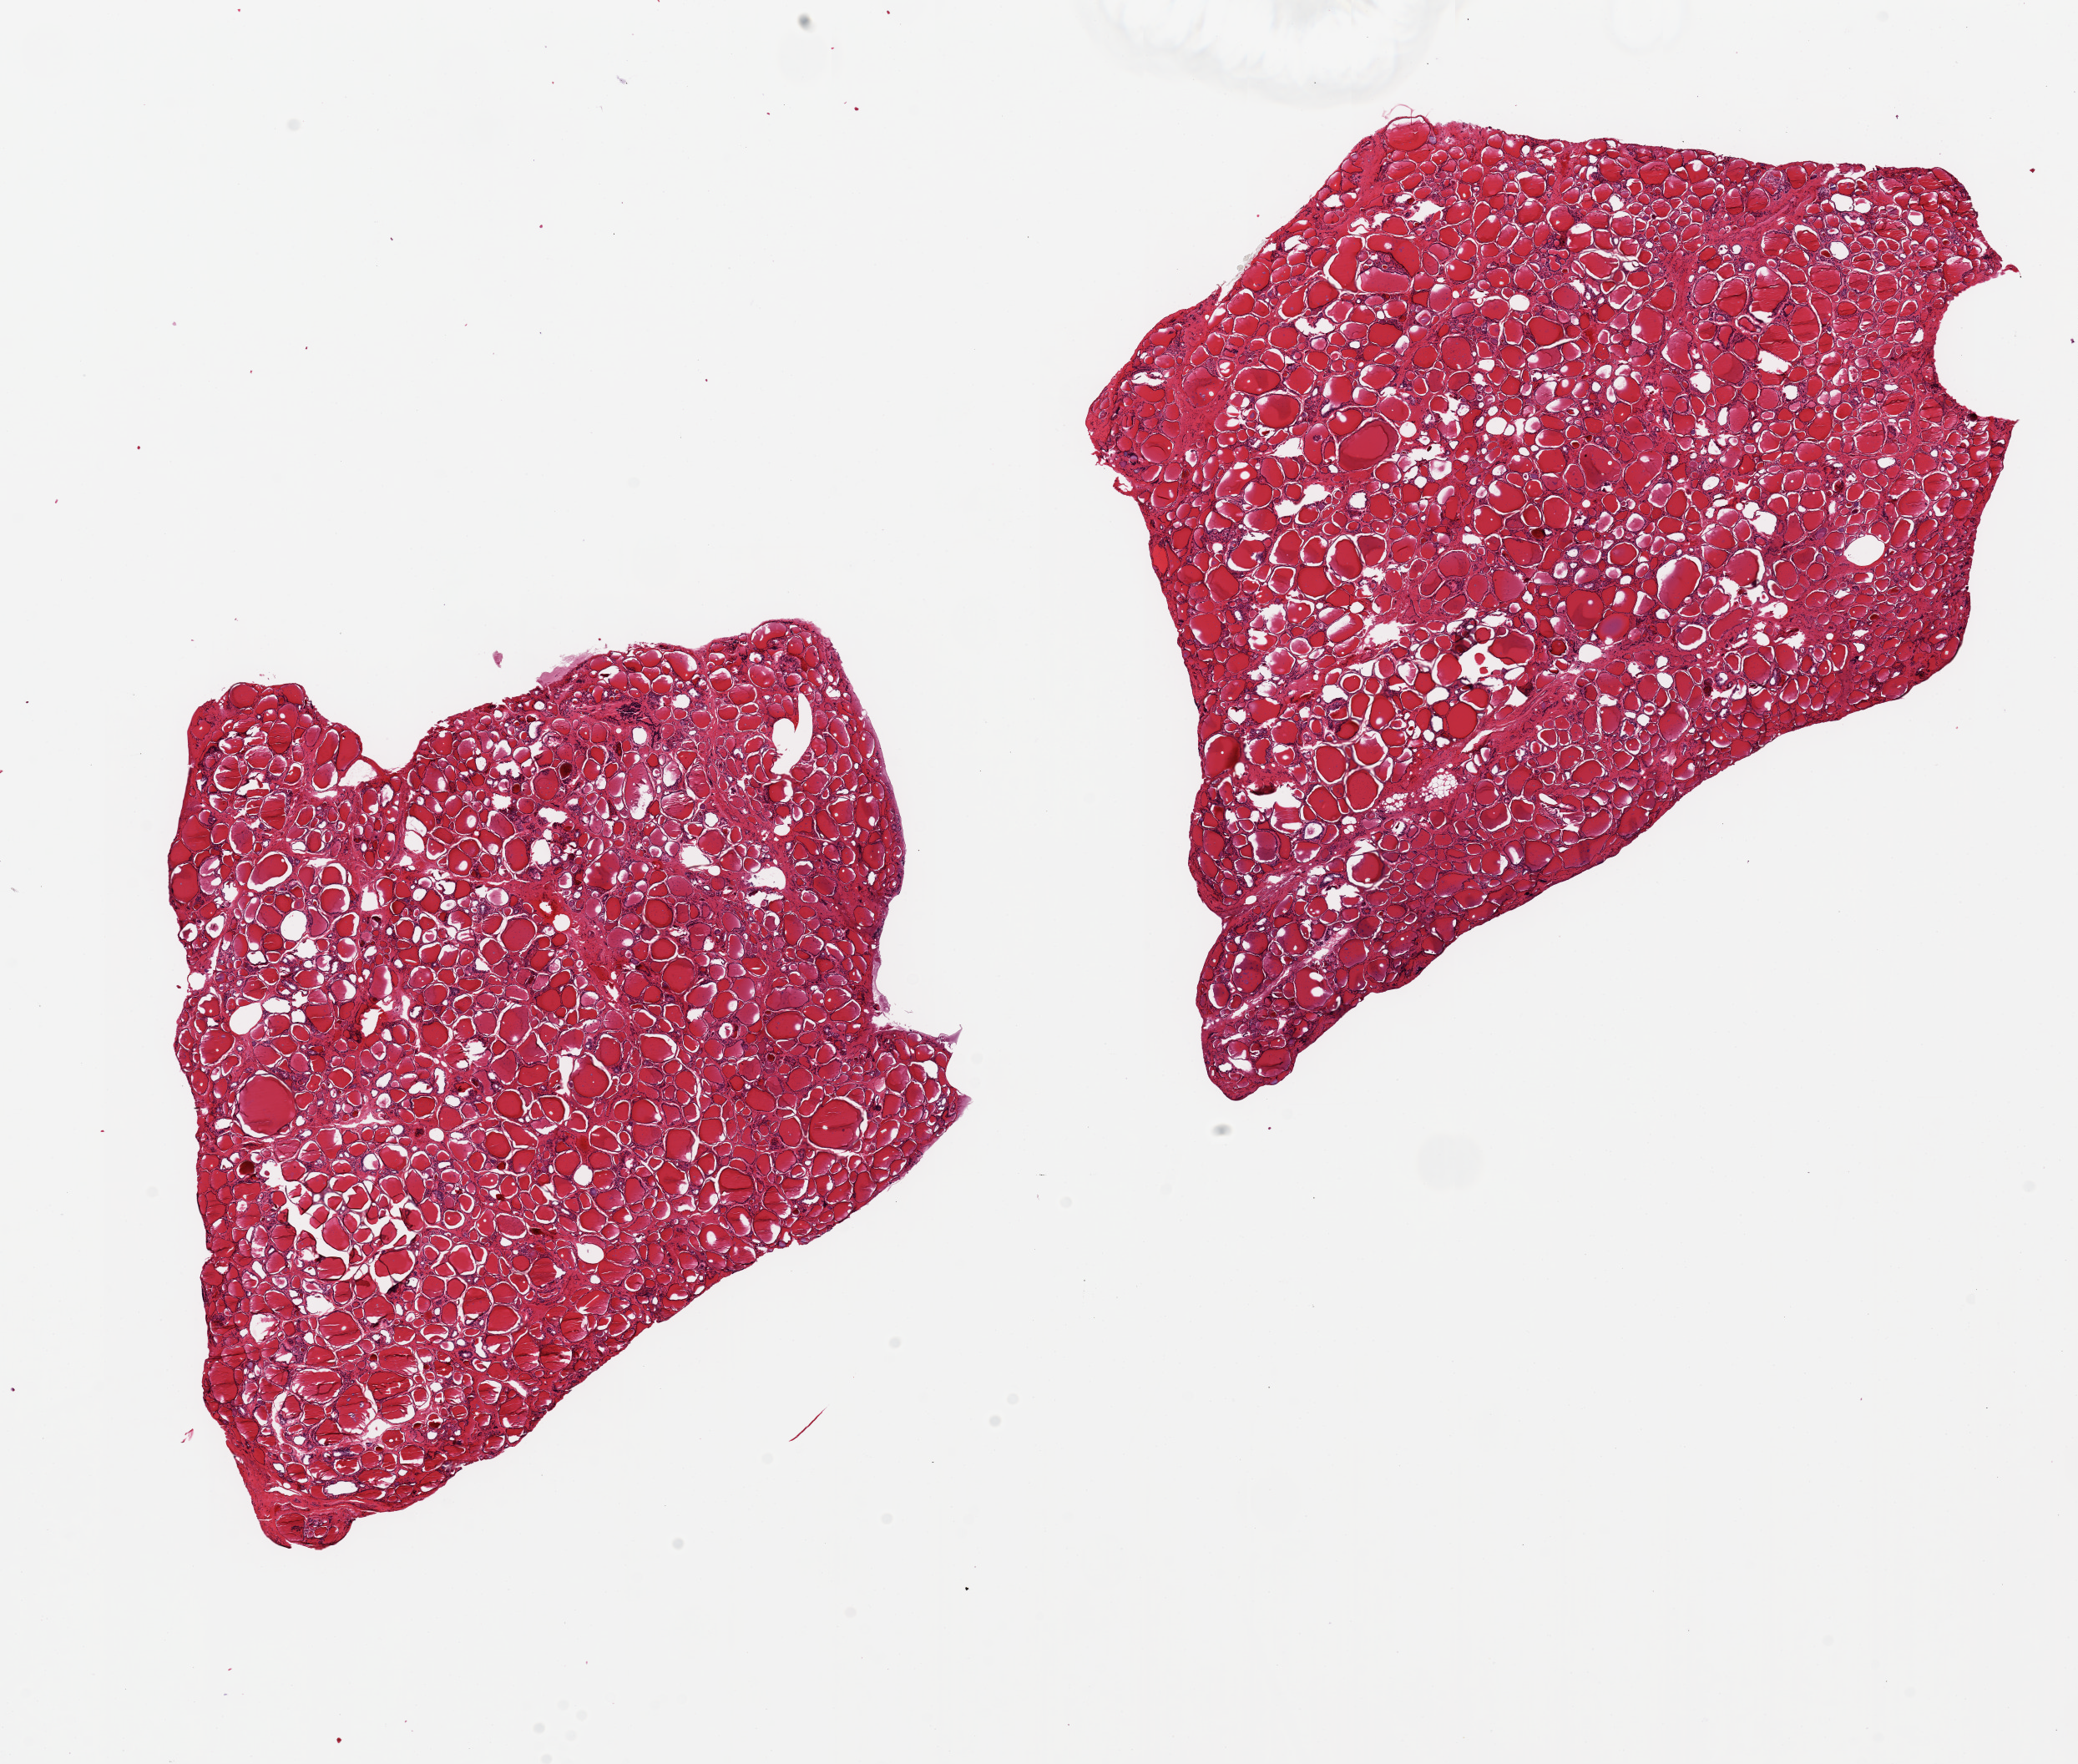
Digitized H&E-stained section, brightfield, low-resolution overview of the scanned area, about 19.7 x 16.7 mm, PAXgene-fixed, paraffin-embedded tissue, section of thyroid (target tissue), donor tissue sample. Donor: male.
Review note (as recorded): 2 pieces, 8x8 & 9x9mm.